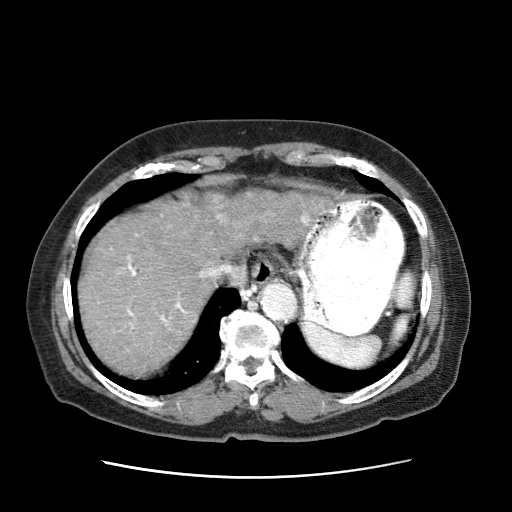
Contrast-enhanced abdominal CT (liver protocol), one axial slice. Position 56 of 63 along the scan axis. 120 kVp. Intravenous contrast given. Soft-tissue window (W 400 / L 40 HU). 512 × 512 image matrix, field of view 360 × 360 mm. Female patient, age 79 years. From the clinical record (not read from this slice): diagnosis: hepatocellular carcinoma (patient treated with transarterial chemoembolisation; whether this scan precedes or follows treatment is not stated here); TNM stage (as recorded): Stage-II; Child-Pugh class: B.
Outlined on this slice (semi-automatic segmentation, software-assisted and operator-edited):
- abdominal aorta: bounding box [x1, y1, x2, y2] px = [260, 283, 296, 321]
- liver parenchyma outside the tumour (the mass and vessels are separate outlines, so this box may not span the whole liver): [78, 192, 249, 379]
- mass: [205, 190, 332, 248]
- liver vessels: [97, 214, 247, 326]